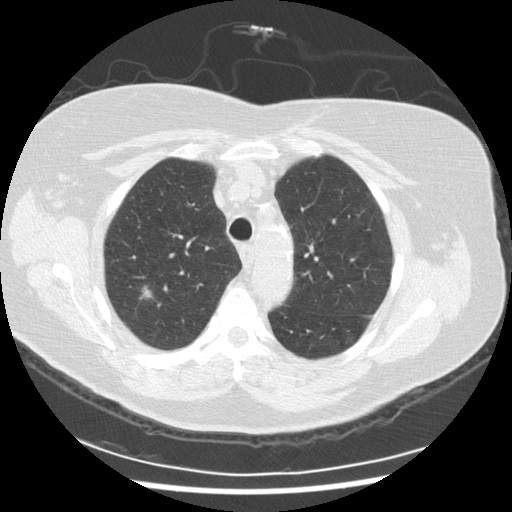
Low-dose screening chest CT, one axial slice; slice 202 of 254 in the series (ordered by position); reconstruction kernel STANDARD; lung window (W 1500 / L -600 HU); 2.5 mm slice thickness; 512 × 512 image matrix, field of view 360 × 360 mm.
Outlined on this slice (outlined manually by an expert reader):
- lesion 1 (tumor, upper lobe of right lung): box from (x=139, y=286) to (x=152, y=299) px